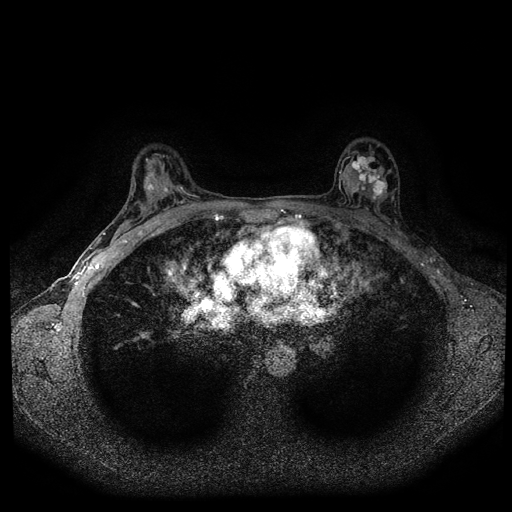
Breast MRI (dynamic contrast-enhanced, multi-phase), one axial slice. Position 58 of 108 along the scan axis. Dynamic contrast-enhanced series, time point 2 of 5 at this slice position (early post-contrast). 1.5 T. TE 2.7 ms, TR 5.5 ms. 2 mm slice thickness. 512 × 512 image matrix, field of view 320 × 320 mm. Female patient, age 36 years.
Structures marked on this image (semi-automatically segmented with operator editing):
- breast lesion (labelled 'tumour' in the annotation; benign lesions carry a separate 'benign' label): box from (x=345, y=150) to (x=389, y=204) px